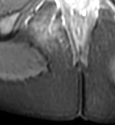
MRI of an extremity soft-tissue mass, one axial slice; slice 34 of 49 in the series (ordered by position); STIR; MR volume resampled by the dataset authors to the PET/CT grid (not the native acquisition matrix); 3.27 mm slice thickness; 115 × 125 image matrix, field of view 112 × 122 mm. Female patient. From the clinical record (not read from this slice): histological type: epithelioid sarcoma; grade: intermediate; site of the primary tumour: right buttock.
Structures marked on this image (expert contour drawn on MRI and transferred to this co-registered scan by the dataset authors):
- gross tumour volume including surrounding oedema: bounding box <38,18,57,38> (left, top, right, bottom; pixels)